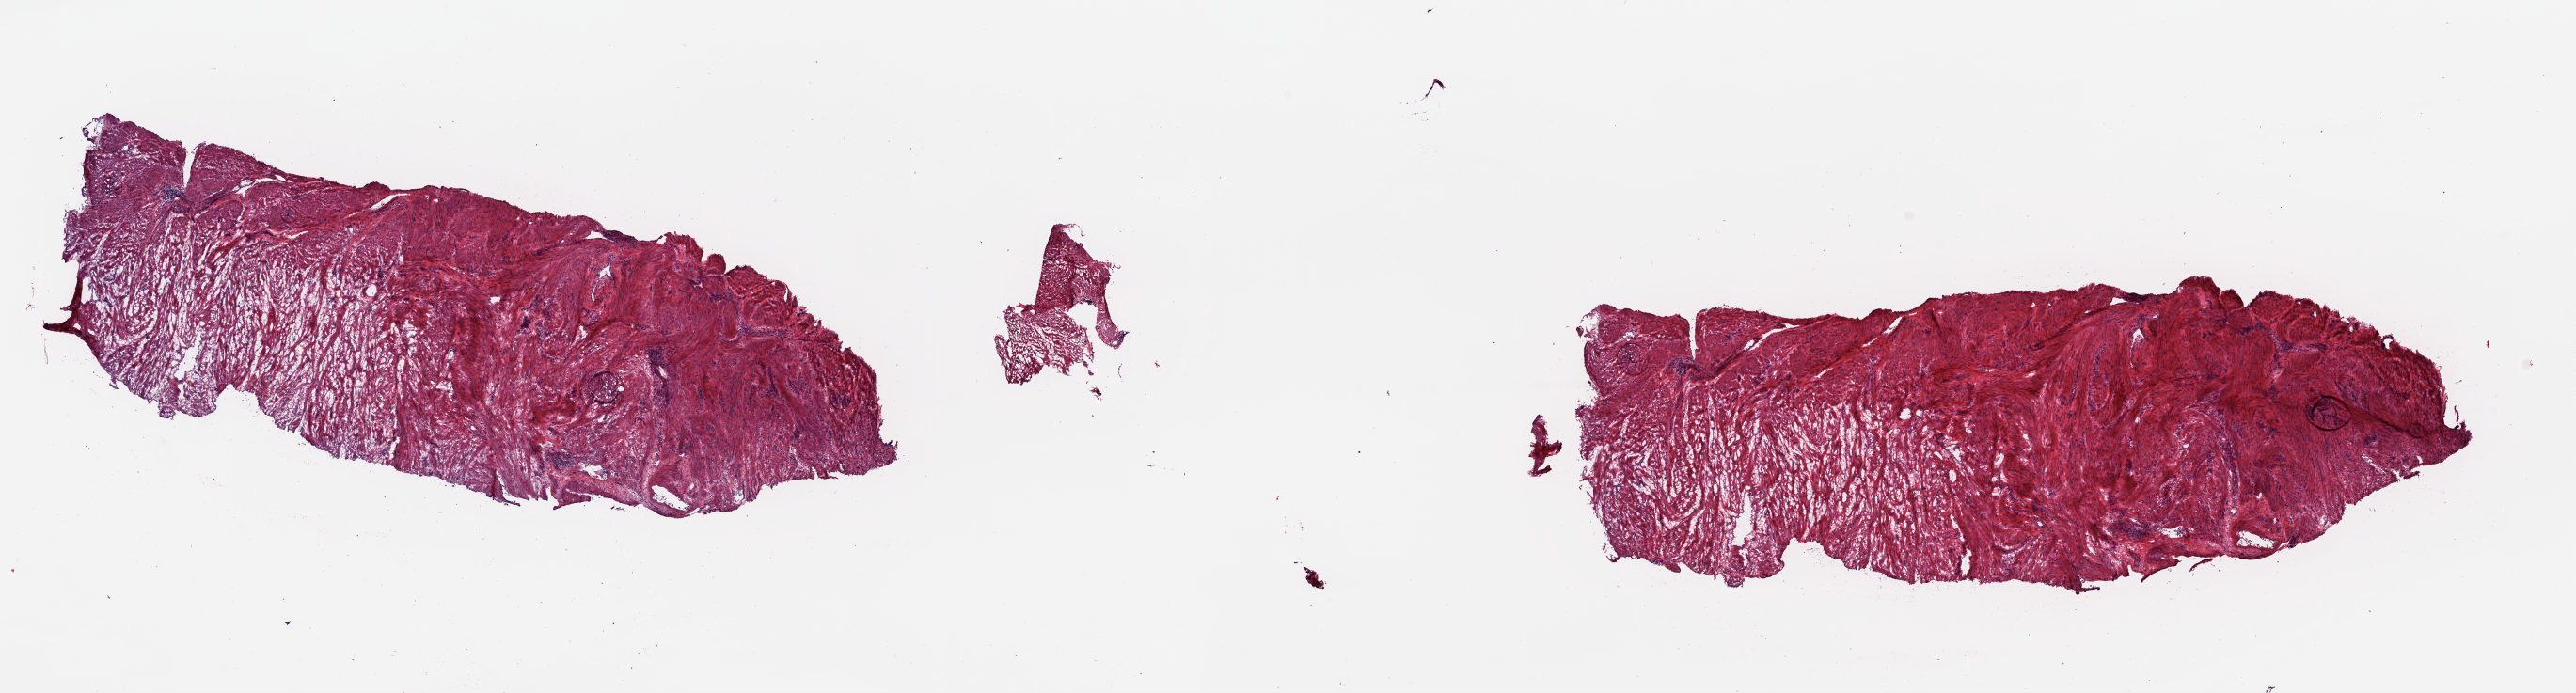
Hematoxylin and eosin (H&E) stained whole-slide image, a low-resolution overview of the entire scanned area, about 21.6 x 5.8 mm (slide scanned at 20x); frozen section from the top of the tissue portion; uterus, solid tissue normal (non-tumour tissue) sample. Female, age 53 years at initial diagnosis. Slide review estimates, as recorded: tumour cells 0%, tumour nuclei 0%, normal cells 100%, stromal cells 0%, necrosis 0%. Inflammatory infiltration, as recorded: lymphocyte infiltration 5%, monocyte infiltration 0%, neutrophil infiltration 0%.
• this section: solid tissue normal (non-tumour) sample from the same patient
• patient diagnosis: Endometrioid adenocarcinoma, NOS